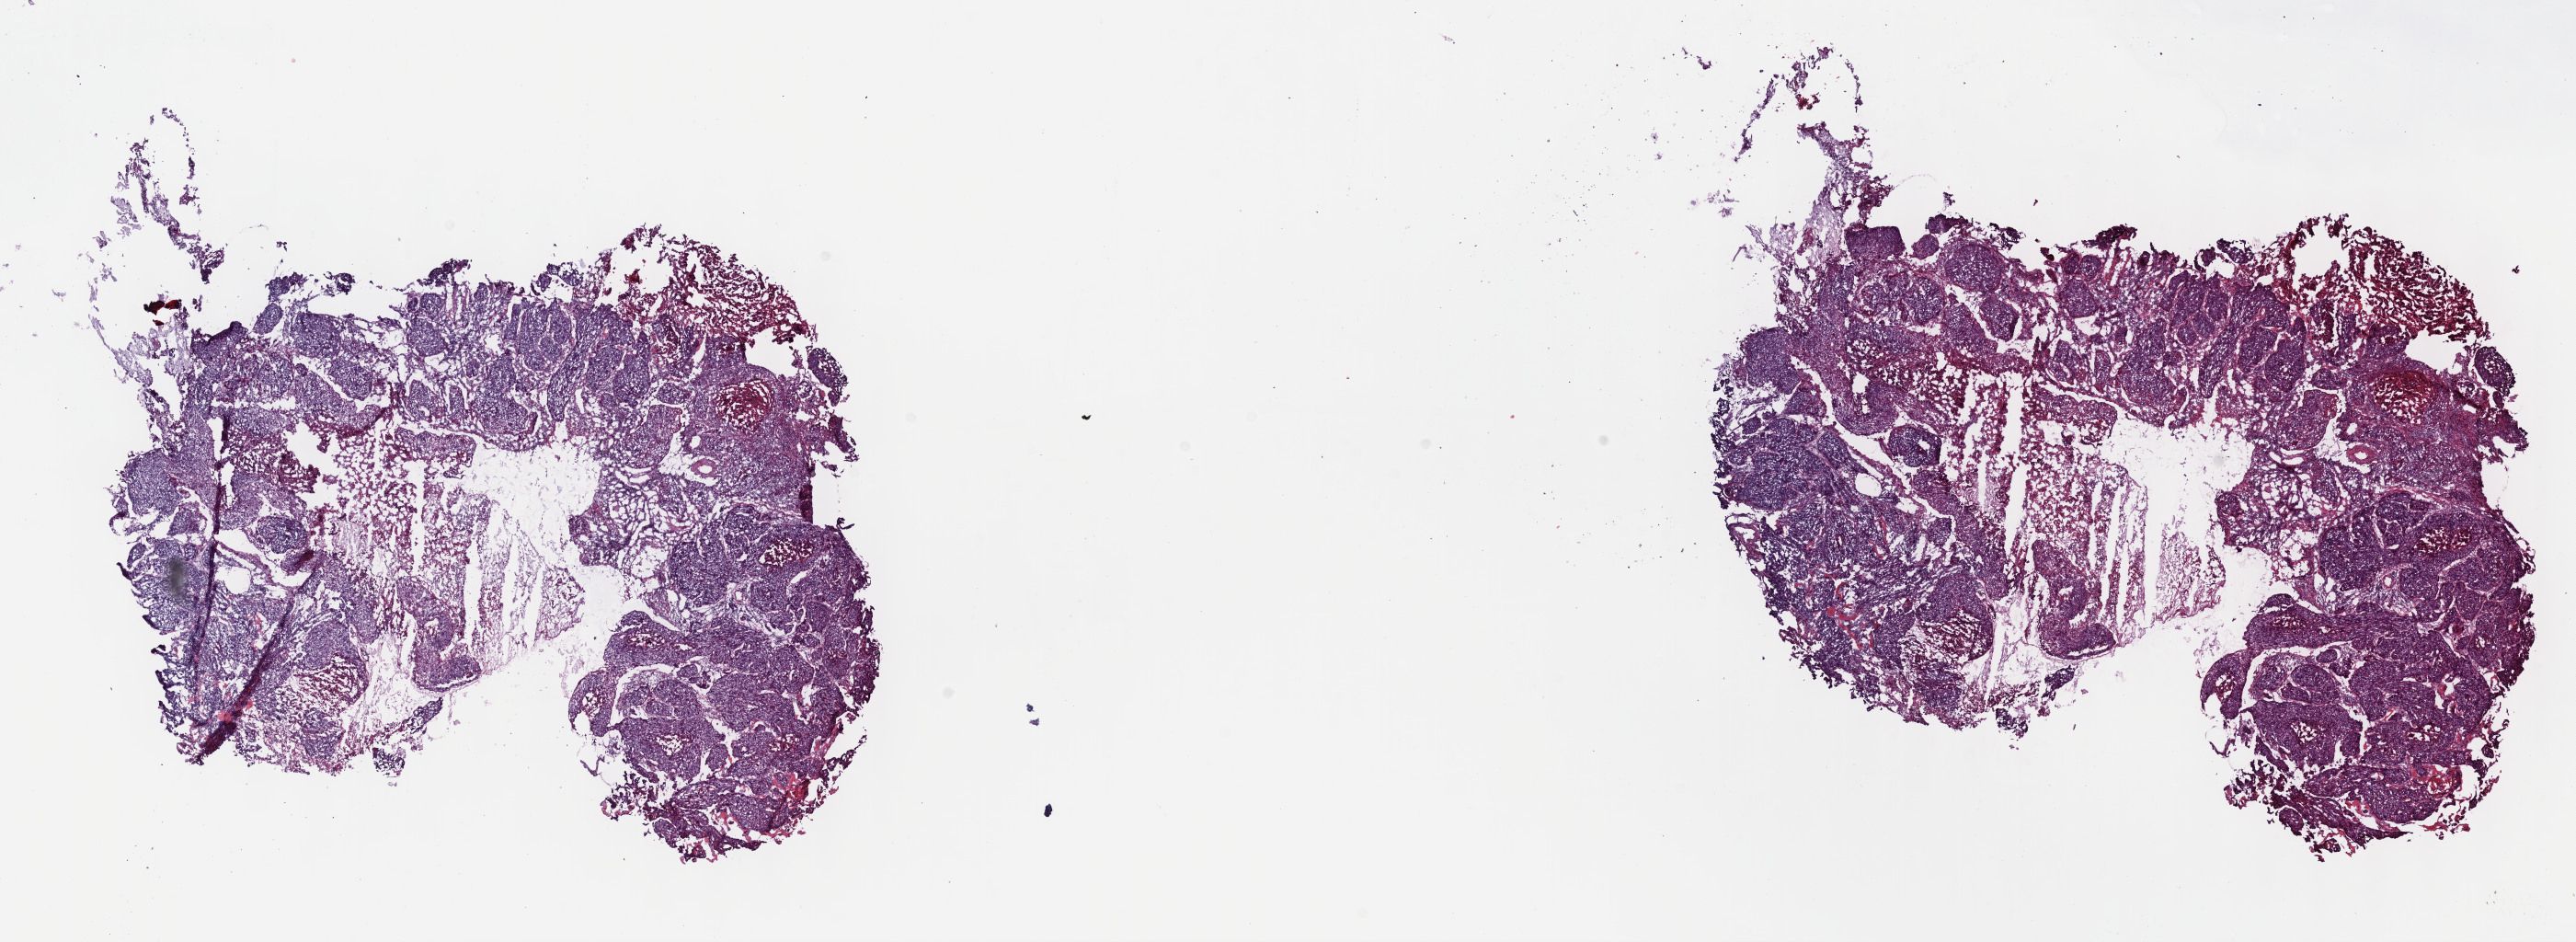
Digitized Hematoxylin and eosin (H&E) stained tissue section (whole slide), whole scanned area (about 22.7 x 8.3 mm) shown as a low-resolution overview, frozen section from the top of the tissue portion, sample: primary tumour, cervix. Female patient; age at initial diagnosis 67 years. Histologic grade: G2 (moderately differentiated). Slide review estimates, as recorded: tumour cells 85%, tumour nuclei 90%, normal cells 0%, stromal cells 15%, necrosis 0%. Inflammatory infiltration, as recorded: lymphocyte infiltration 0%, monocyte infiltration 0%, neutrophil infiltration 0%.
Diagnosis: Squamous cell carcinoma, NOS (cervix uteri). FIGO stage: IIIB.